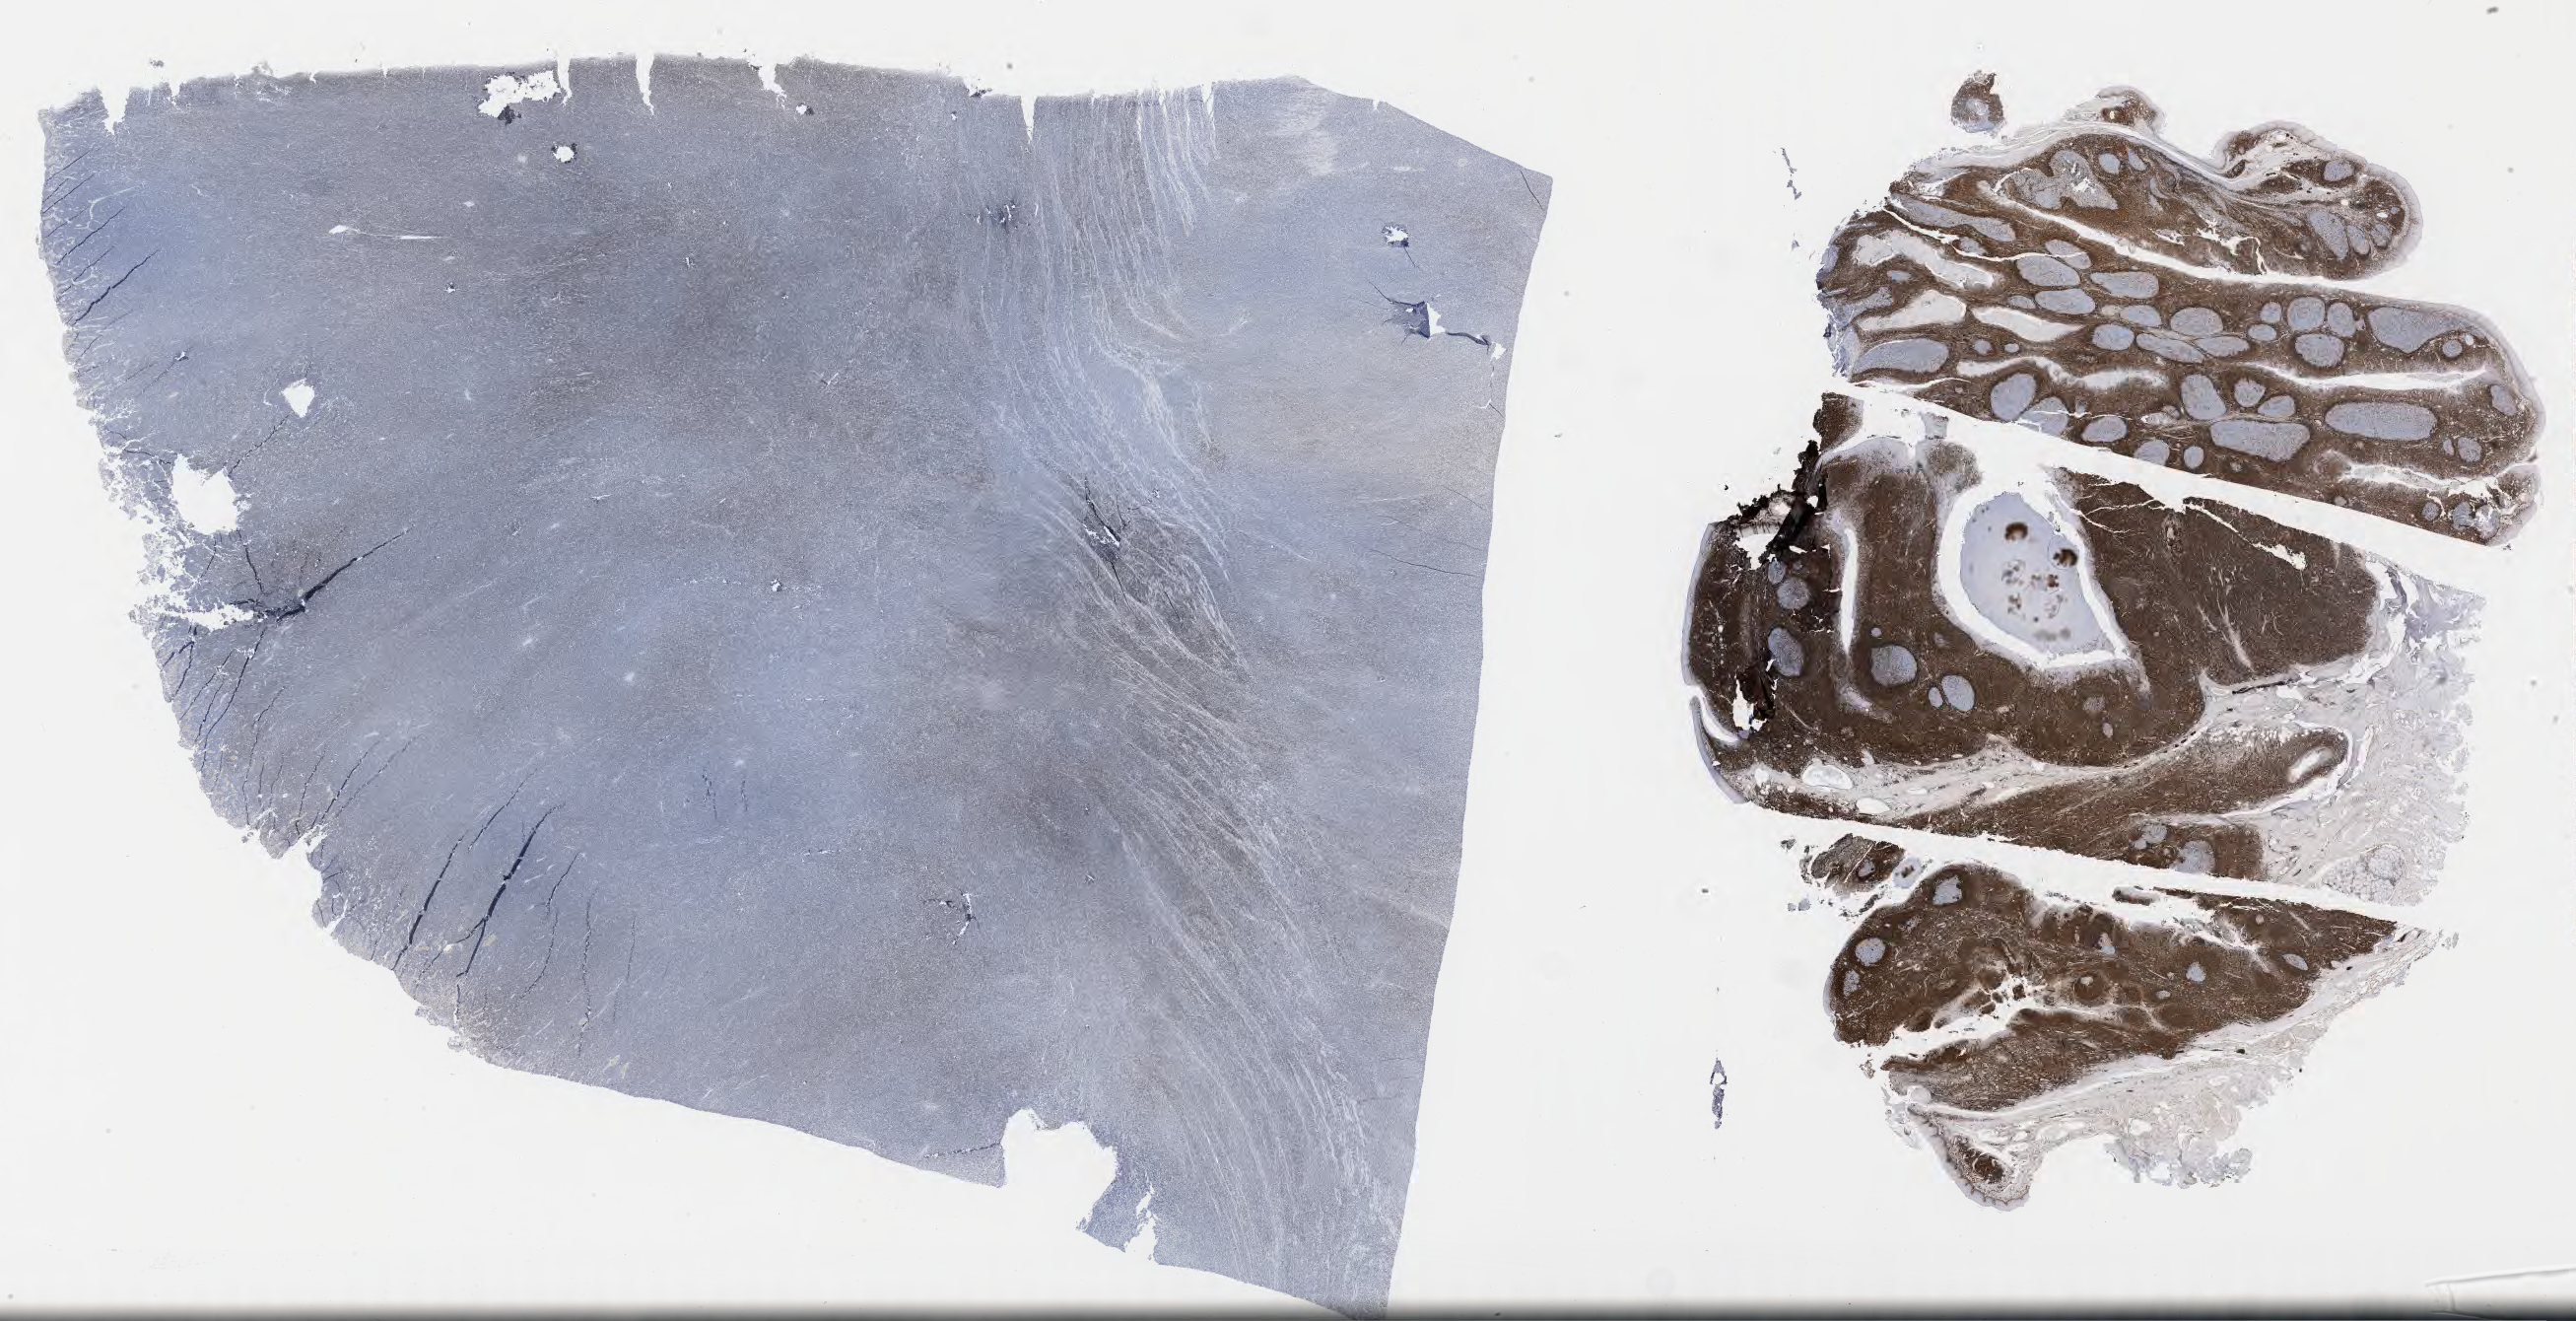
IHC for BCL2, whole-slide image — whole scanned area (about 42.3 x 21.7 mm) shown as a low-resolution overview, tumor tissue. Patient: male, age 17 years.
Diagnosis: Burkitt lymphoma, NOS.